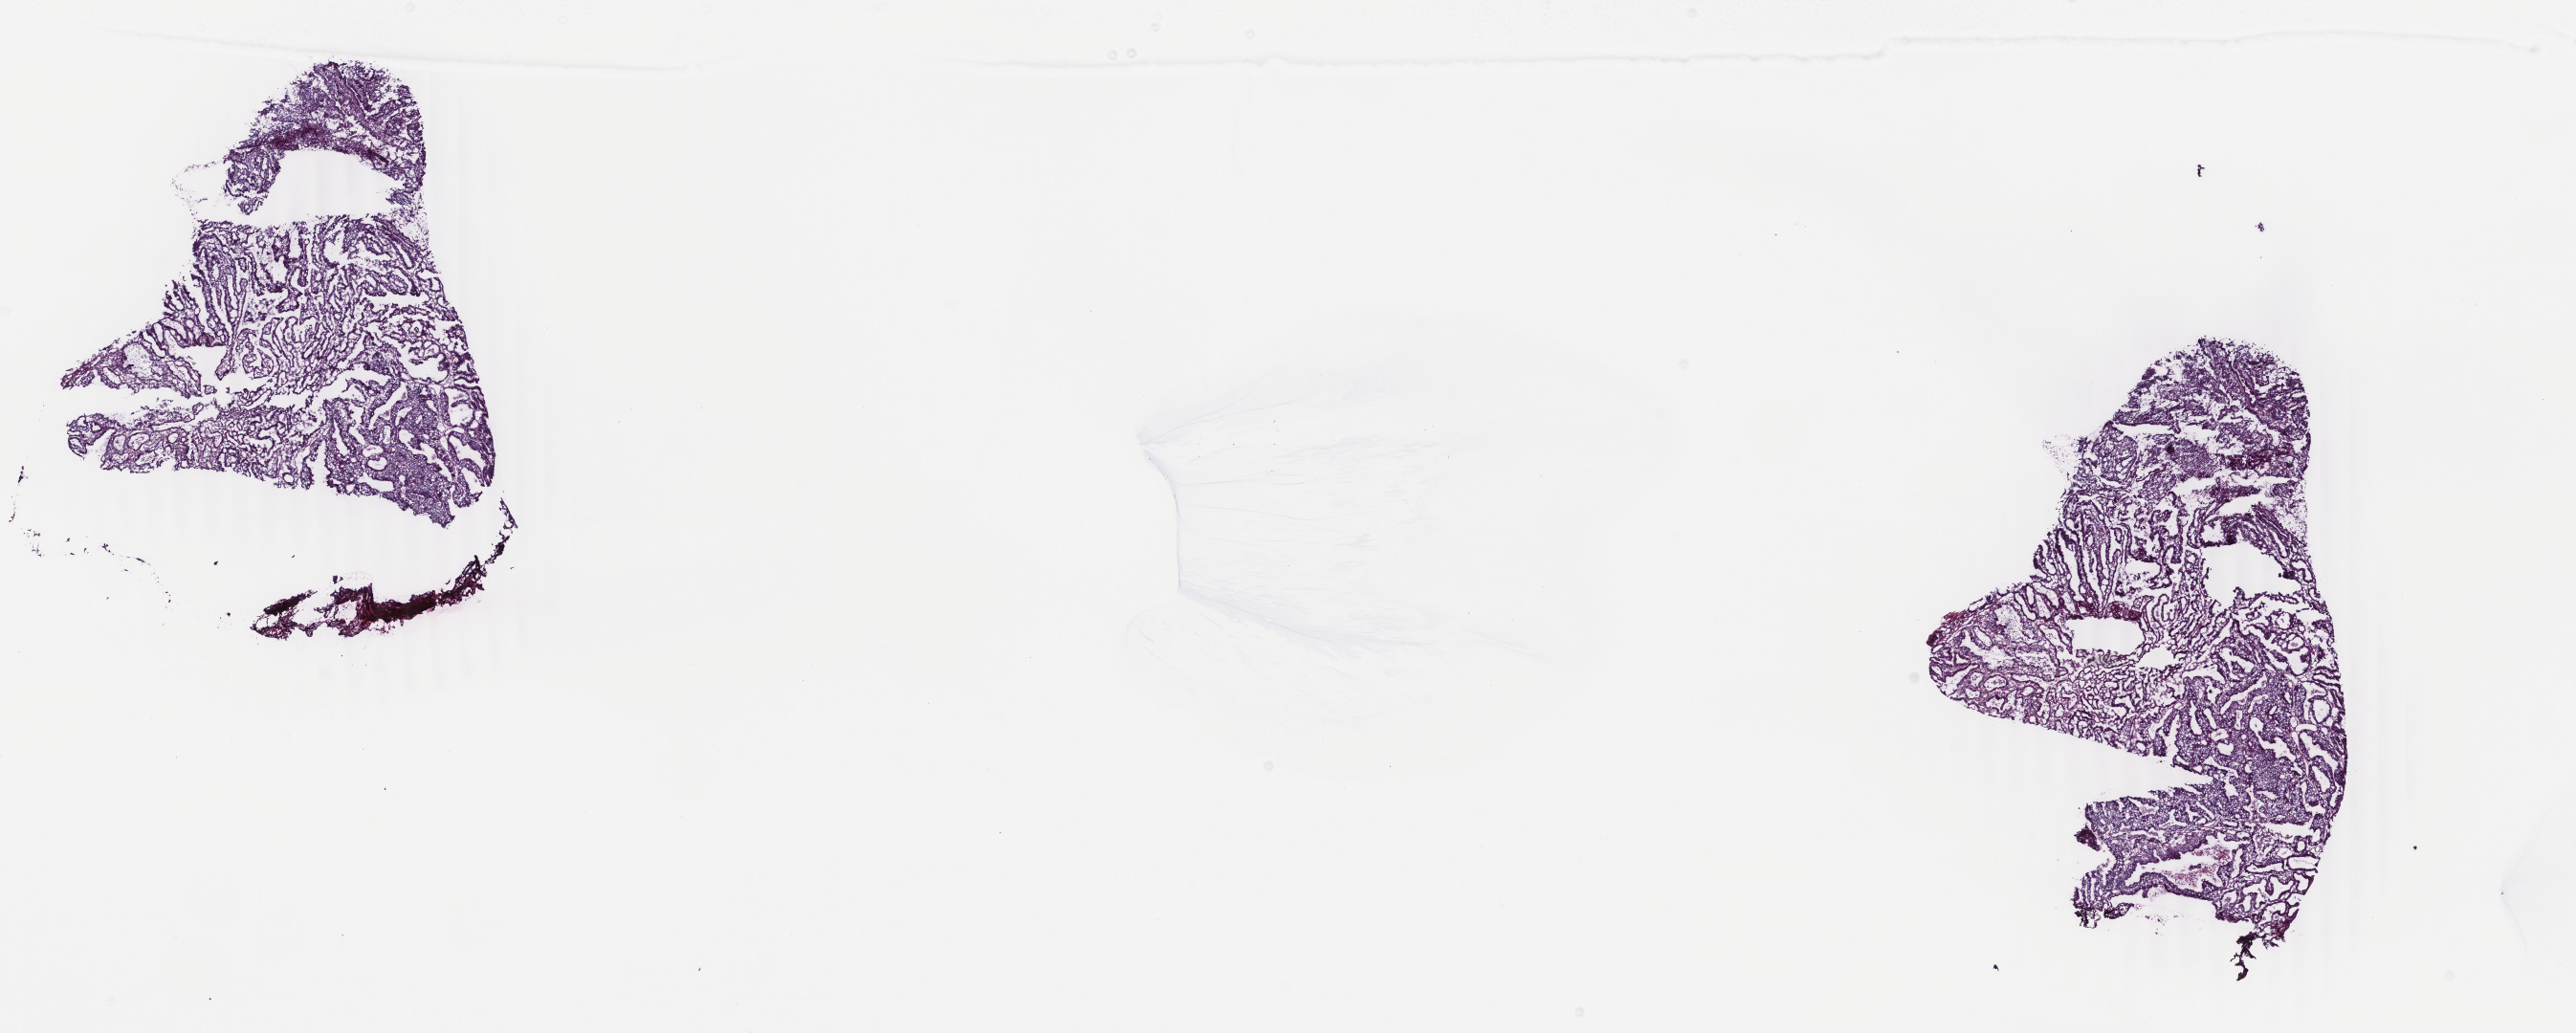
Whole-slide histology image, H&E-stained, whole scanned area (about 21.4 x 8.6 mm, from a 40x scan) shown as a low-resolution overview; frozen section from the top of the tissue portion; uterus, primary tumour sample. Patient: female, age at initial diagnosis 60 years. Histologic grade: G1 (well differentiated). Slide review estimates, as recorded: tumour cells 70%, tumour nuclei 70%, normal cells 10%, stromal cells 15%, necrosis 5%. Inflammatory infiltration, as recorded: lymphocyte infiltration 40%, monocyte infiltration 10%, neutrophil infiltration 40%.
FIGO stage: IA. Pathologic diagnosis: Endometrioid adenocarcinoma, NOS (endometrium).